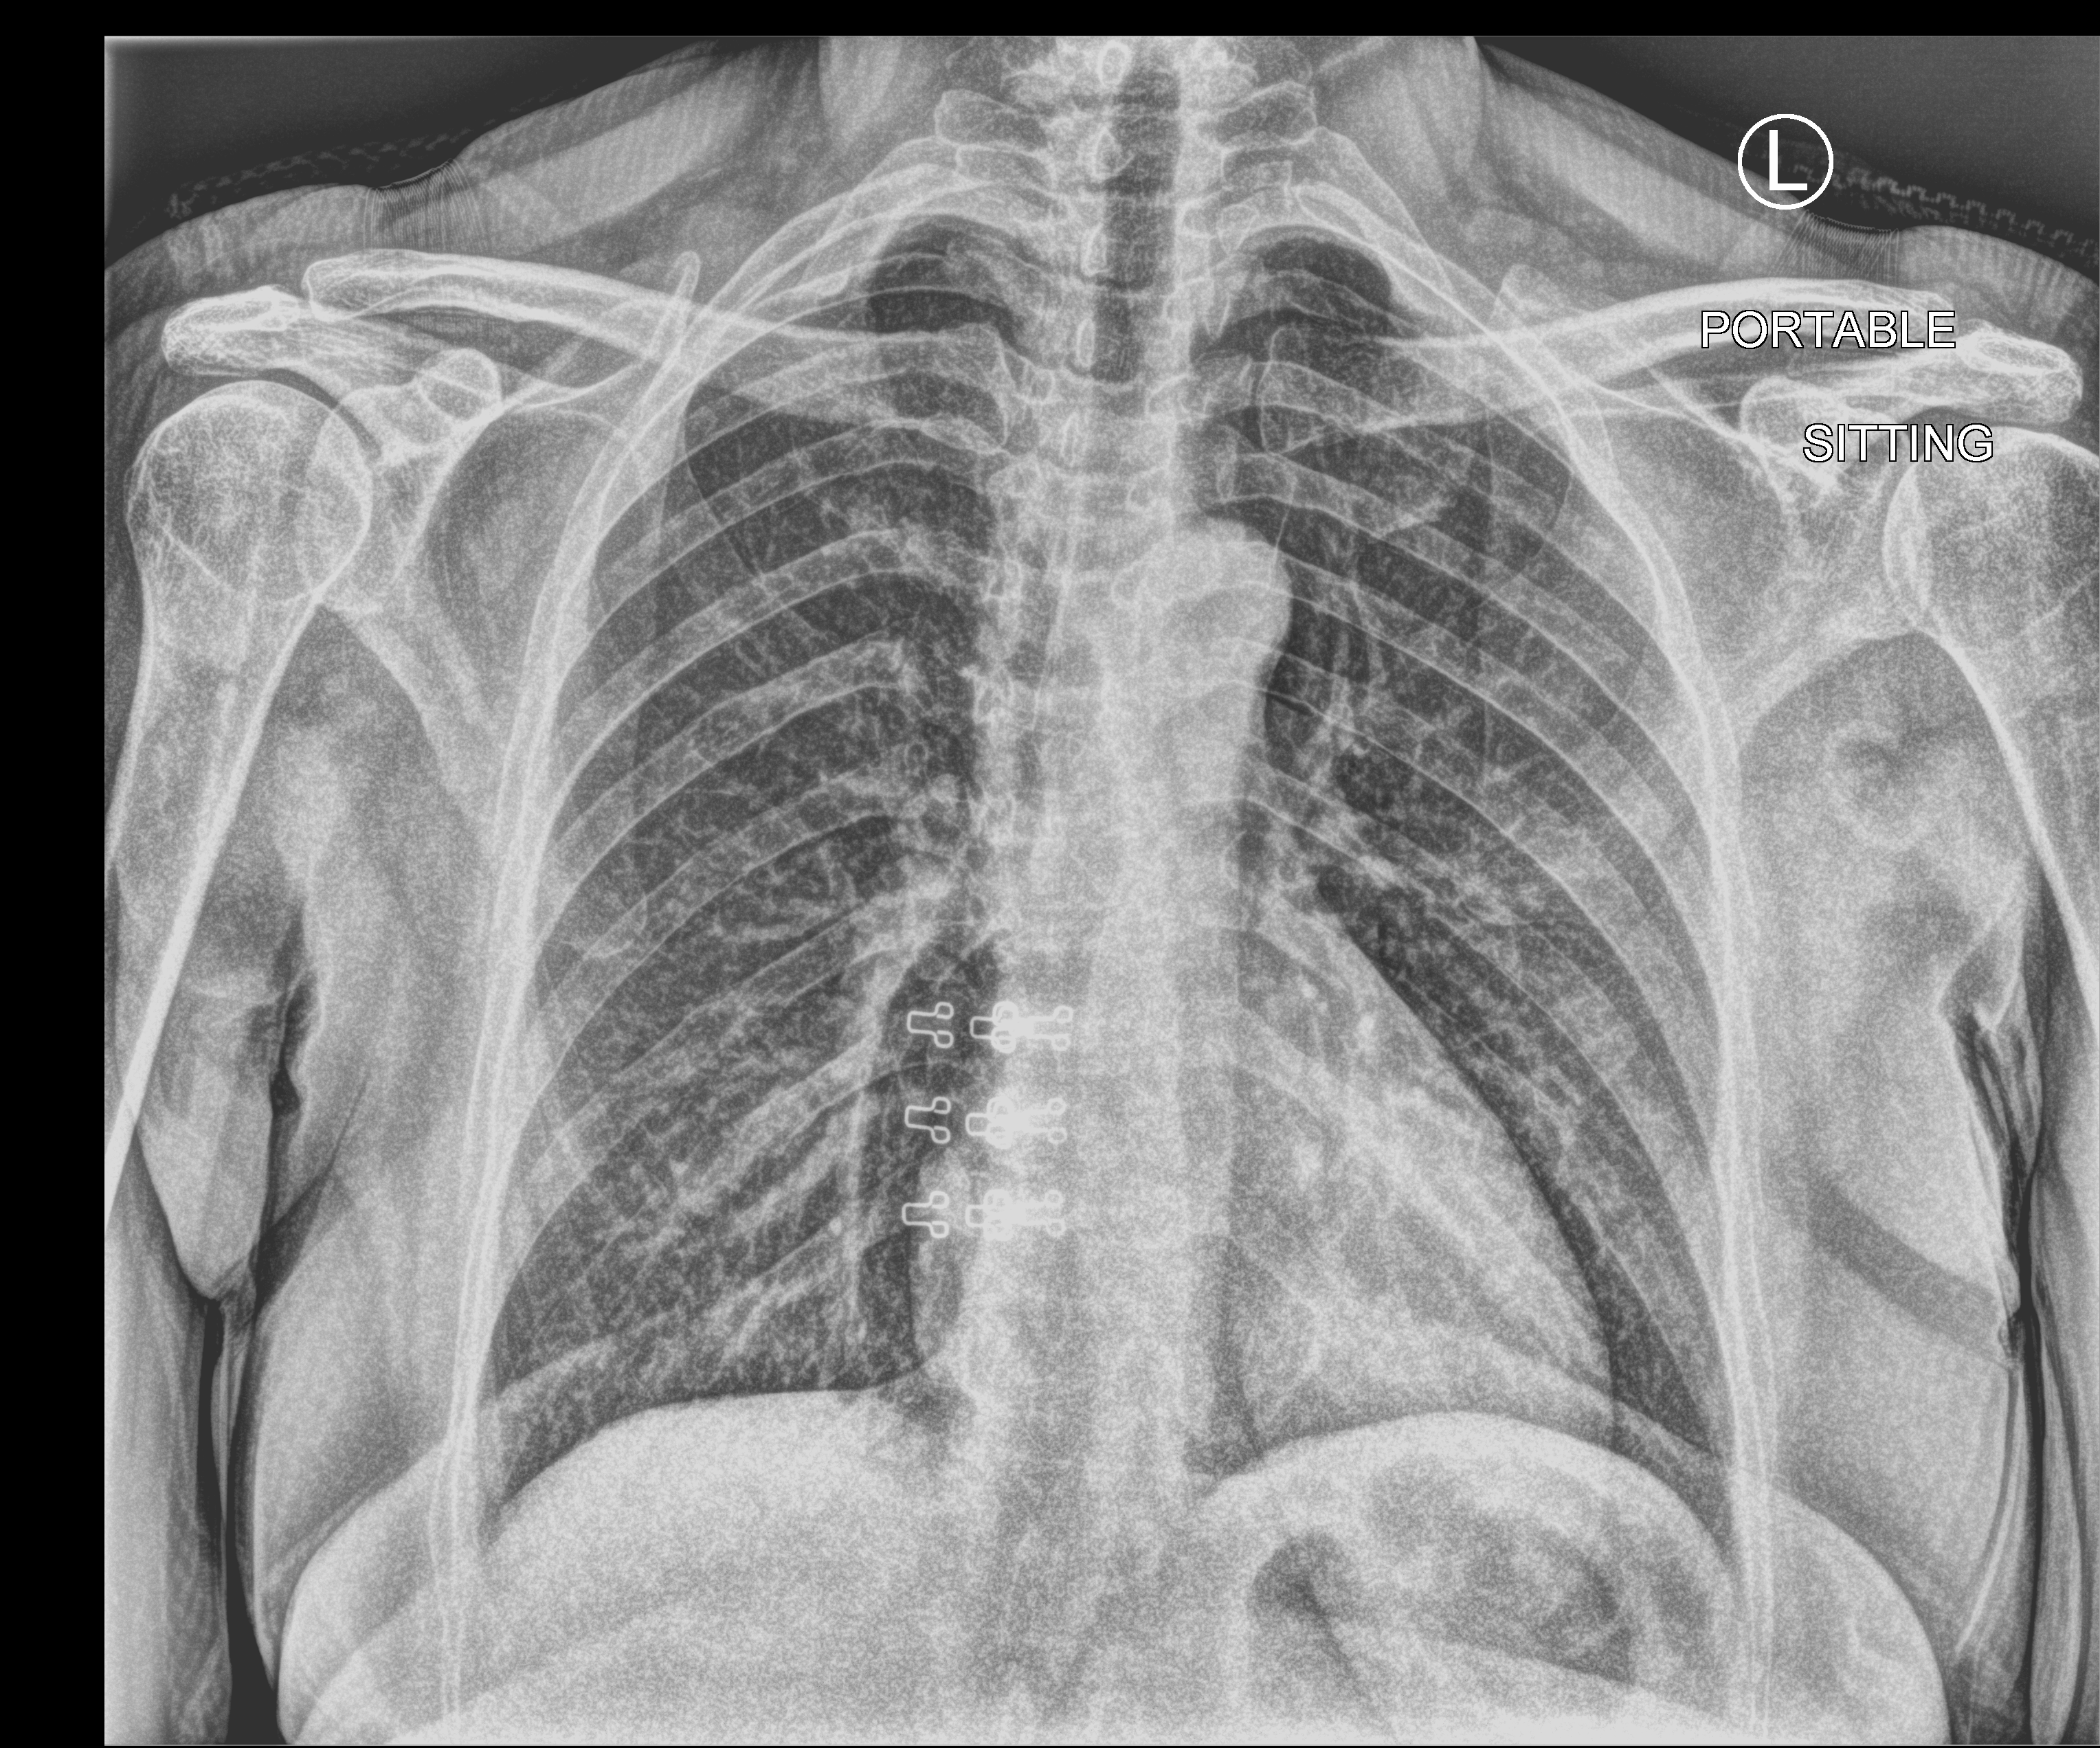
Bedside chest radiograph (computed radiography); anteroposterior (AP) projection. Female patient hospitalised with COVID-19, age 18–59 years.
Hospital-stay facts (about this admission, not read from this image; timing relative to this image not recorded):
- diabetes (admission record): no